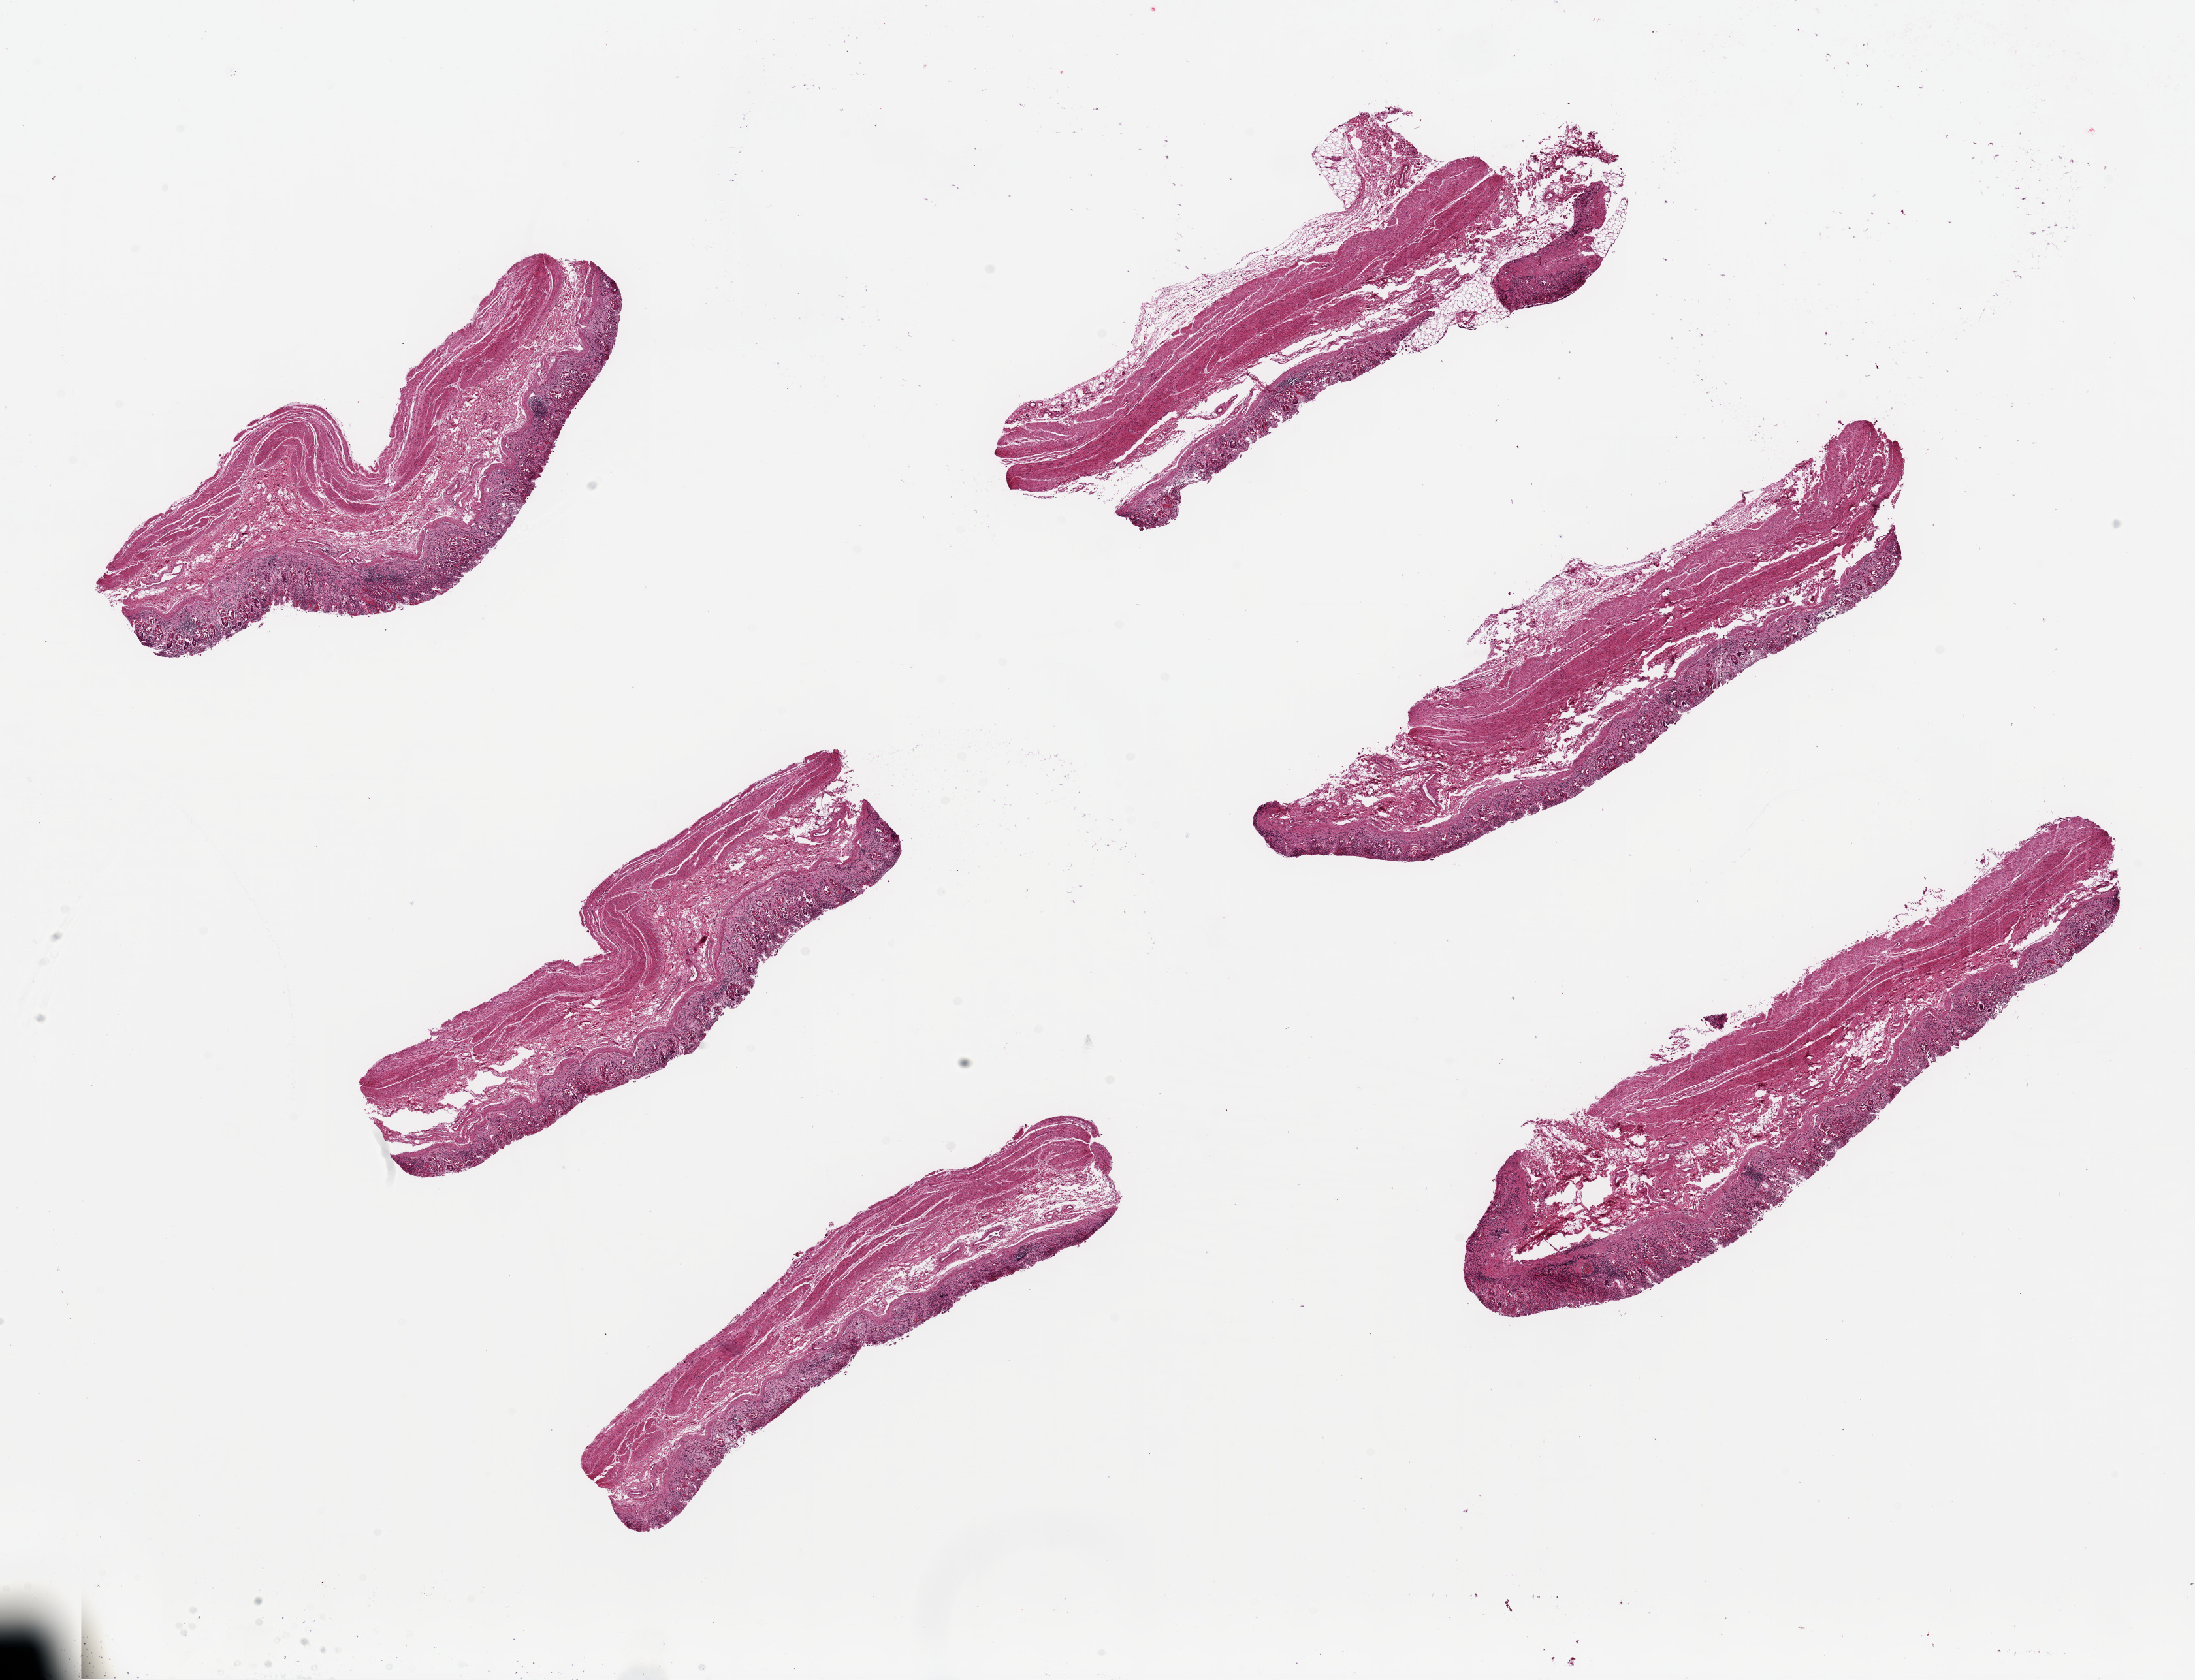
Digitized haematoxylin and eosin-stained section — a low-resolution overview of the entire scanned area, about 26.6 x 20.3 mm (slide scanned at 20x). PAXgene-fixed paraffin-embedded (PFPE) section. Section of stomach (target tissue). Tissue donor sample. Donor: male.
Review note (as recorded): 6 ~8x3mm pieces. Epithelium totally autolyzed; mucosal stroma partly sloughed. Areas of poor fixation with tears/holes.